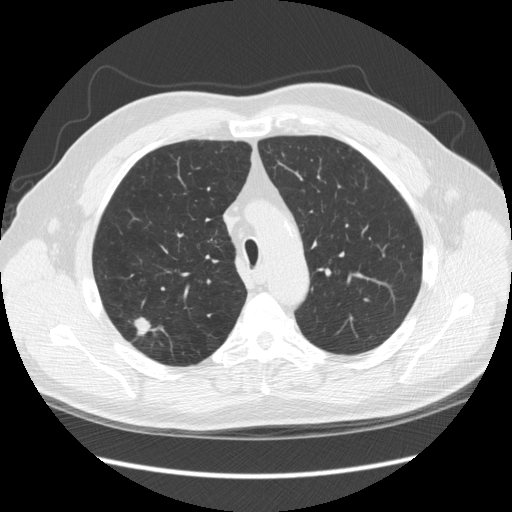
Chest CT (low-dose screening protocol), one axial image. Third screening round (two years after baseline). Lung window (W 1500 / L -600 HU). 2.5 mm slice thickness. Slice 64 of 248 in the series. Male participant, aged 64 years at enrolment. Former smoker at enrolment.
Expert-annotated lung lesion, bounding box [x1, y1, x2, y2] px = [117, 314, 169, 357]. The screening reader recorded 4 non-calcified nodules or masses ≥4 mm on this exam; which of them this box marks is not recorded. Official screen result: positive, other. Participant outcome: lung cancer diagnosed 15 days after this screen — adenocarcinoma, NOS, right upper lobe, moderately differentiated (G2), stage IA (AJCC 6th edition), 14 mm at pathology.